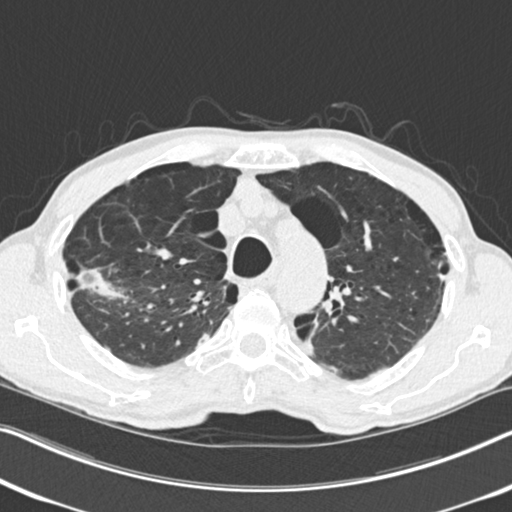
Axial slice from a low-dose chest CT screening exam, second annual screen, lung window (W 1500 / L -600 HU), standard (soft-tissue) reconstruction kernel (B30f), slice 62 of 251 in the series. Male participant, aged 71 years at enrolment. Current smoker at enrolment.
• Lesion marked by an expert reader, box from (x=66, y=246) to (x=139, y=318) px.
• The screening reader recorded 4 non-calcified nodules or masses ≥4 mm on this exam (right upper lobe, right upper lobe, right upper lobe, left upper lobe); which of them this box marks is not recorded.
• Participant outcome: lung cancer diagnosed 83 days after this screen — adenocarcinoma, NOS, right upper lobe, well differentiated (G1), stage IA (AJCC 6th edition), 30 mm at pathology.